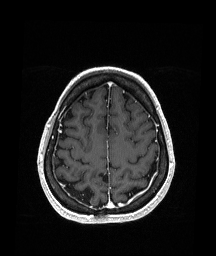
Brain MRI from a brain-tumour surgery series, one axial slice. Slice 55 of 151 in the series (ordered by position). T1-weighted post-contrast. 1.05 mm slice thickness. 216 × 256 image matrix. Case-level facts recorded for this patient, not image findings: histopathology: Oligodendroglioma; WHO grade: 2; IDH mutation: yes.
Annotated regions visible in this slice (expert manual segmentation):
- previous resection cavity: bounding box (x1, y1, x2, y2) in pixels: (99, 171, 109, 181)